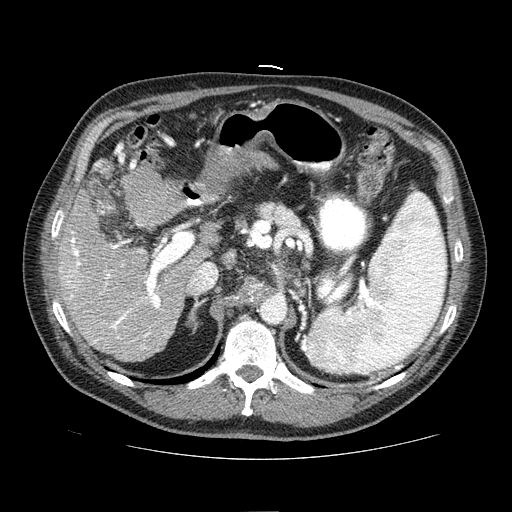
Contrast-enhanced abdominal CT (liver protocol), one axial slice; position 42 of 81 along the scan axis; one of 2 acquisitions stored at this slice position; soft-tissue window (W 400 / L 40 HU); 2.5 mm slice thickness; 512 × 512 image matrix. From the clinical record (not read from this slice): diagnosis: hepatocellular carcinoma (patient treated with transarterial chemoembolisation; whether this scan precedes or follows treatment is not stated here); TNM stage (as recorded): Stage-IIIA; Child-Pugh class: A; tumour differentiation: well differentiated; tumour nodularity: multinodular.
Outlined on this slice (semi-automatically segmented with operator editing):
- liver parenchyma outside the tumour (the mass and vessels are separate outlines, so this box may not span the whole liver): bounding box <58,186,190,362> (left, top, right, bottom; pixels)
- liver vessels: <60,231,169,349>